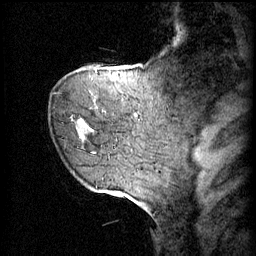
Breast MRI (dynamic contrast-enhanced), one sagittal slice; slice 12 of 60 in the series (ordered by position); 4 images stored at this slice position (order not interpretable as contrast timing); 1.5 T; TE 4.2 ms, TR 11 ms; 2 mm slice thickness; 256 × 256 image matrix. Female patient, age 72 years.
Annotated regions visible in this slice (semi-automatic segmentation, software-assisted and operator-edited):
- analysis volume of interest (the breast-tissue region the enhancement analysis was run in; not a lesion): box from (x=78, y=68) to (x=109, y=153) px
- tumour enhancement mask (voxels above the 70 % enhancement threshold inside the analysis volume of interest): (x=78, y=68)–(x=109, y=139)